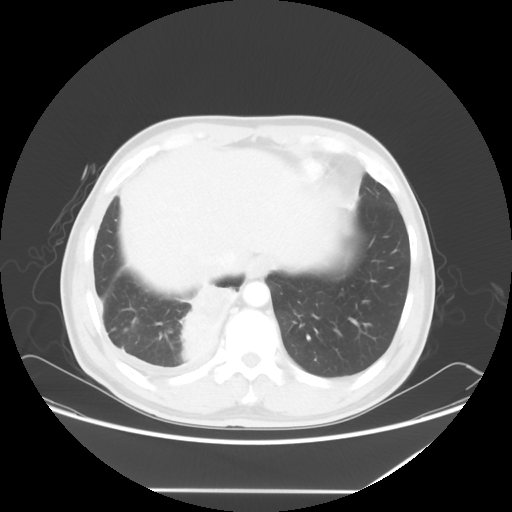
Chest CT, one axial slice; position 13 of 60 along the scan axis; lung window (W 1500 / L -600 HU); 5 mm slice thickness; 512 × 512 image matrix, field of view 419 × 419 mm. Male patient, age 48 years. Case-level facts recorded for this patient, not image findings: clinical TNM (as recorded): T3 N3 M1a.
Outlined on this slice (rectangle marked by the reading radiologist):
- lung tumour (recorded histology: squamous cell carcinoma): box from (x=175, y=276) to (x=239, y=368) px